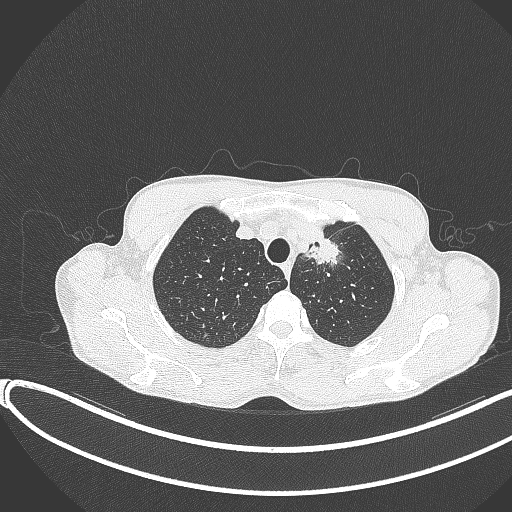
Chest CT, one axial slice. 120 kVp. Lung window (W 1500 / L -600 HU). 1 mm slice thickness. 512 × 512 image matrix, field of view 400 × 400 mm. Male patient, age 58 years. From the clinical record (not read from this slice): clinical TNM (as recorded): T1c N1 M0.
Outlined on this slice (rectangle marked by the reading radiologist):
- lung tumour (recorded histology: adenocarcinoma): bounding box [x1, y1, x2, y2] px = [299, 221, 349, 278]